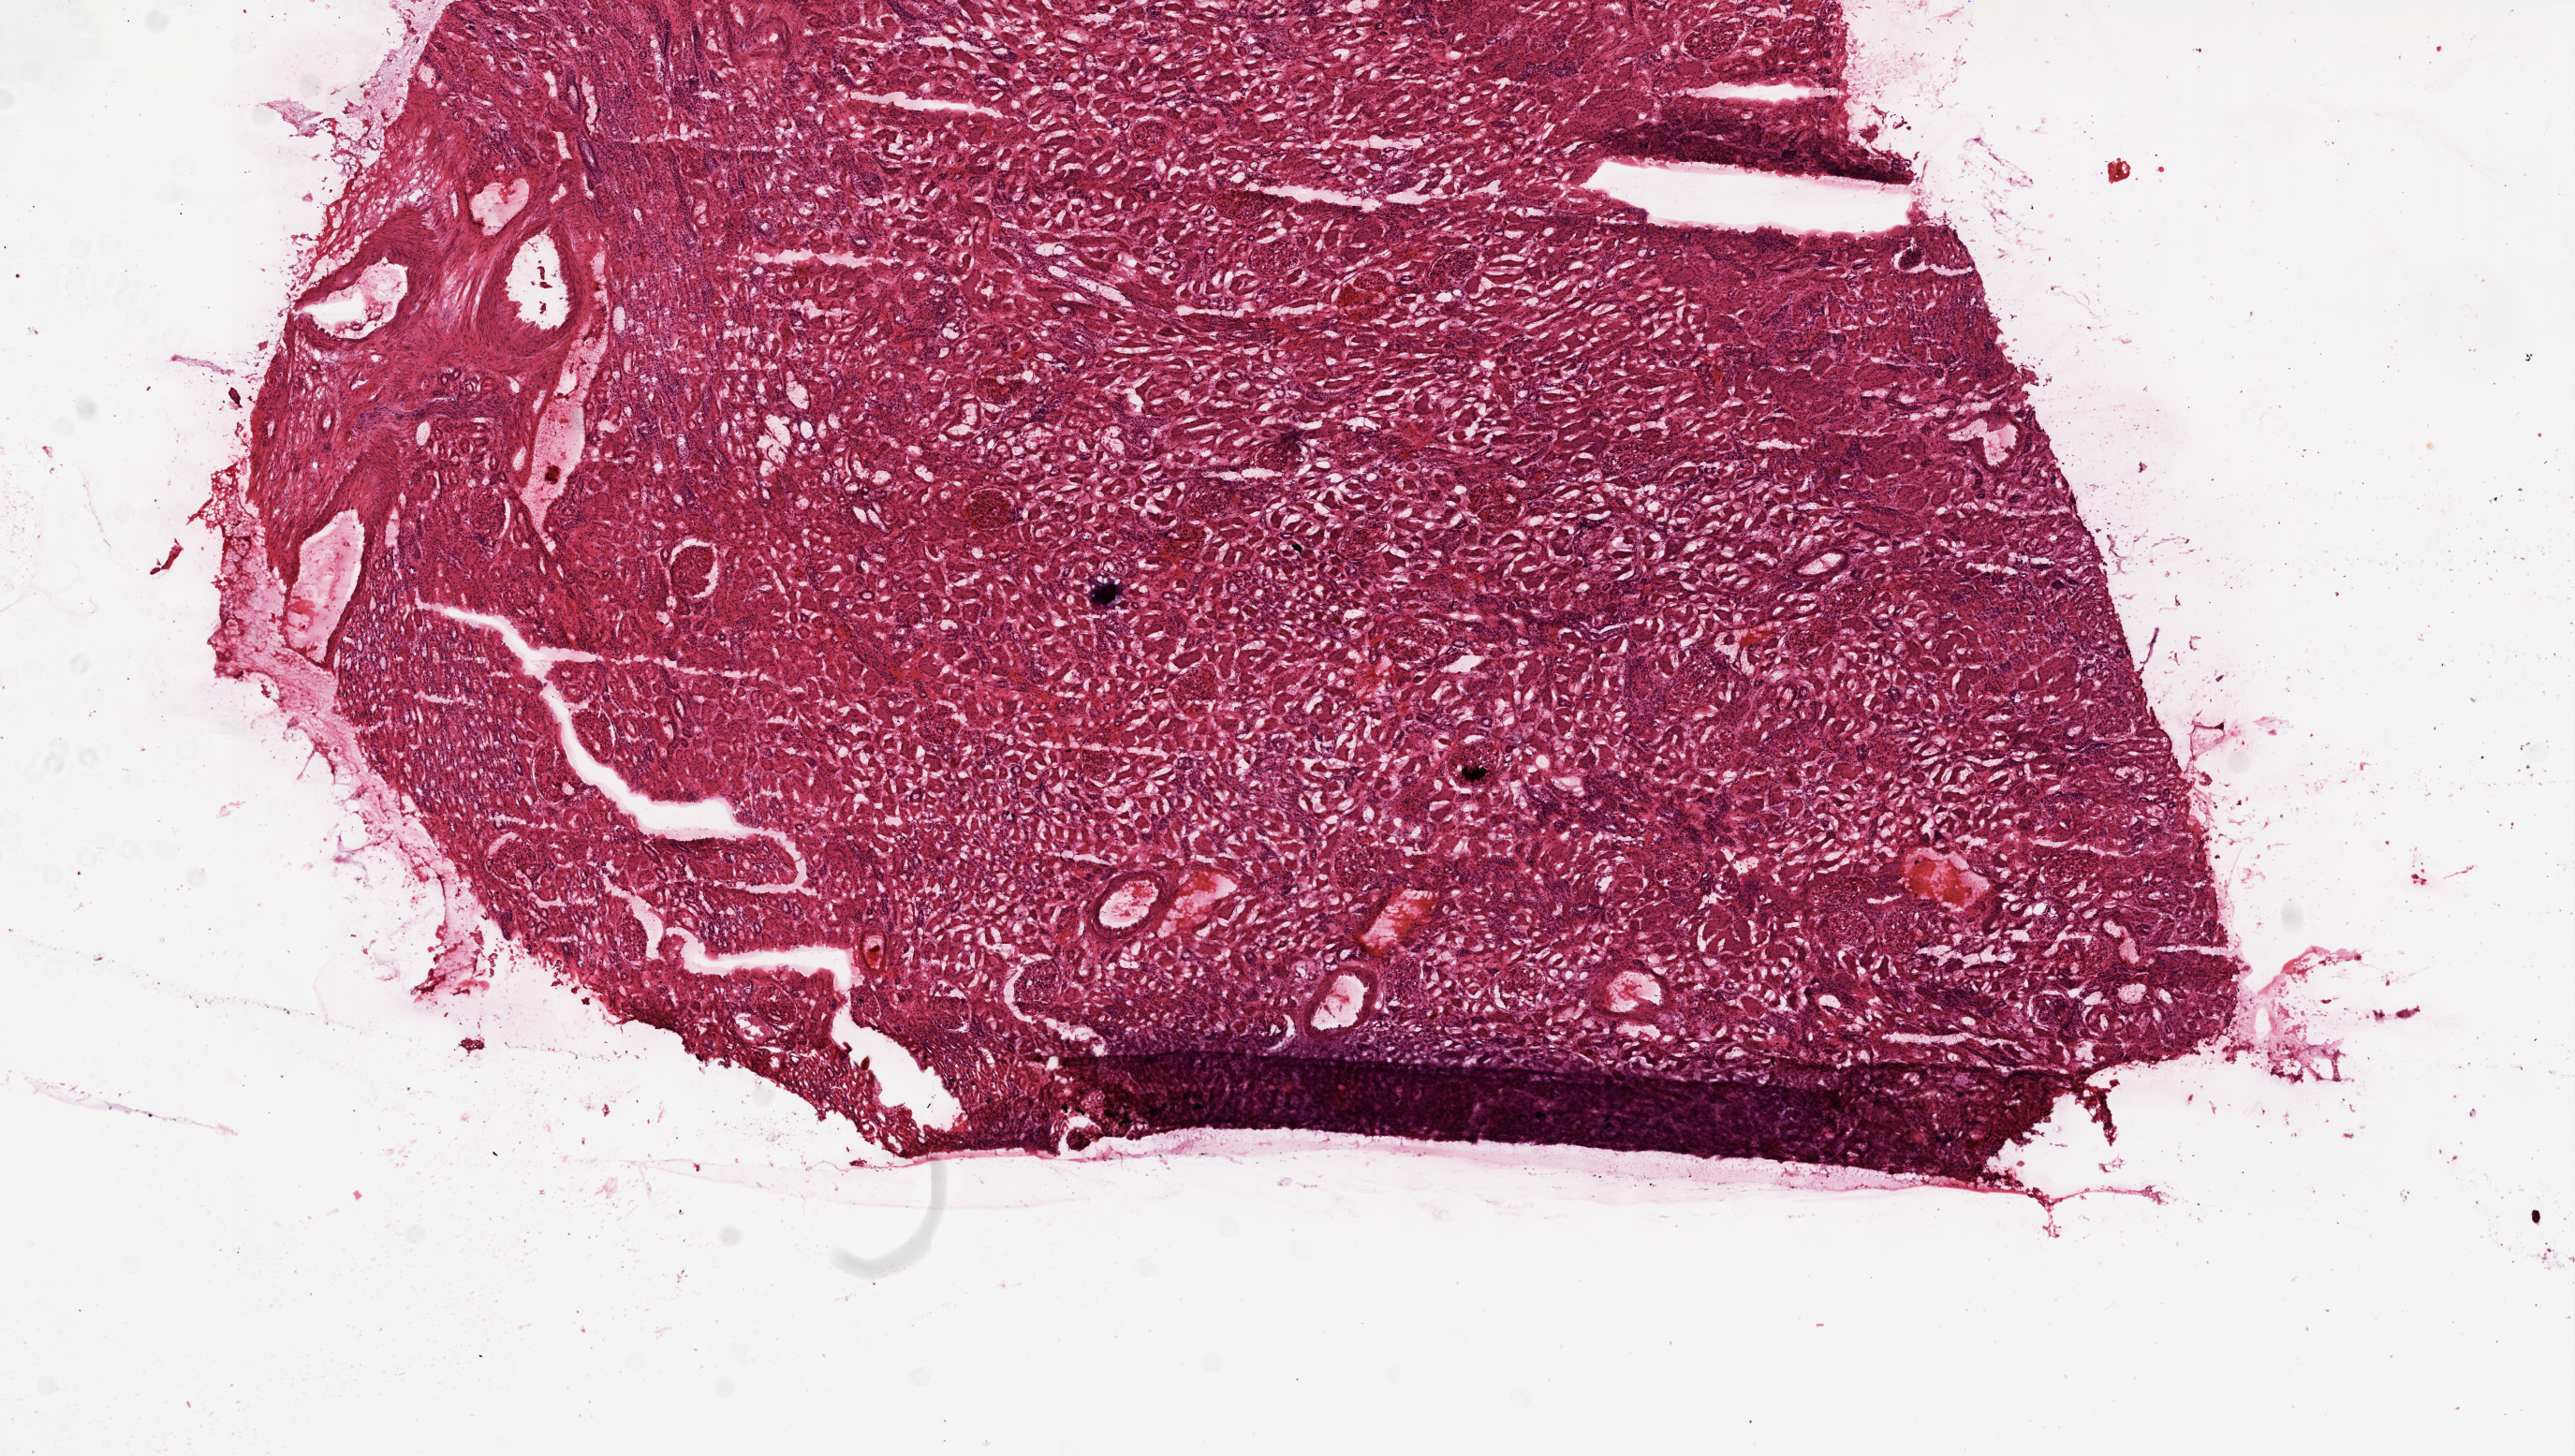
Digitized Hematoxylin and eosin (H&E) stained tissue section (whole slide) — whole scanned area (about 11.0 x 6.2 mm, slide scanned at 20x) shown as a low-resolution overview, frozen section from the top of the tissue portion, sample: solid tissue normal (non-tumour tissue), kidney. Male patient; age at initial diagnosis 51 years.
• this section: solid tissue normal (non-tumour) sample from the same patient
• patient diagnosis: Clear cell adenocarcinoma, NOS